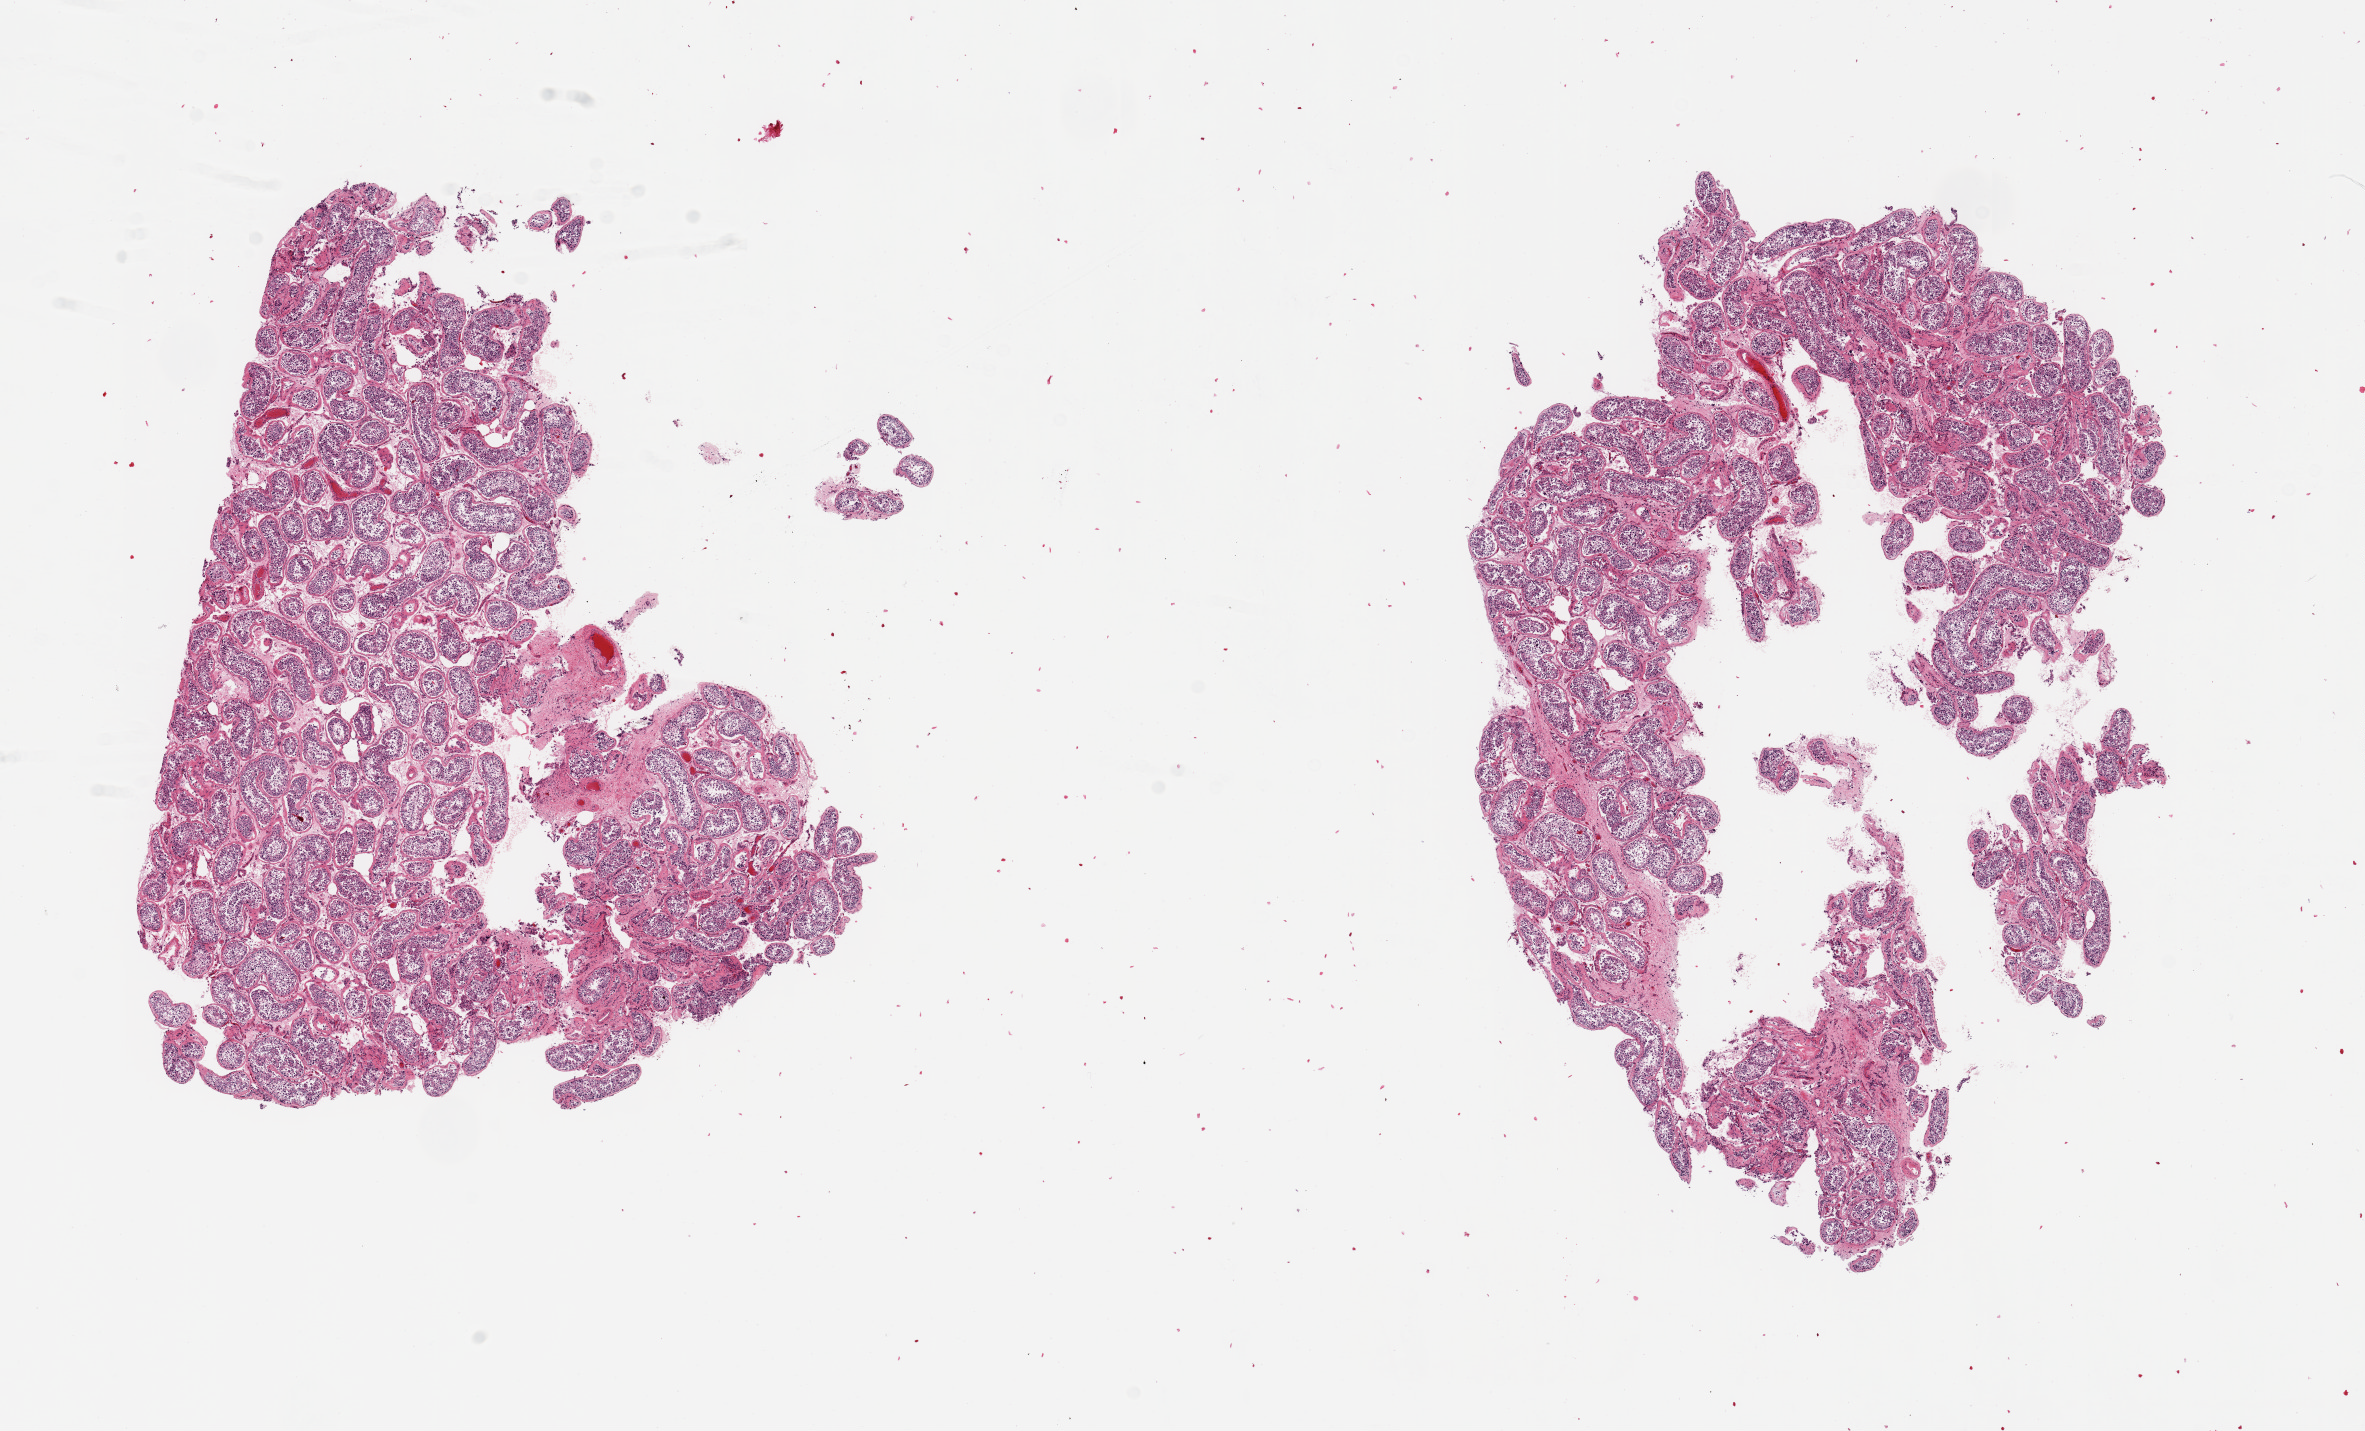
H&E whole-slide image, low-resolution overview of the scanned area, about 18.7 x 11.3 mm (from a 20x scan); PAXgene-fixed, paraffin-embedded tissue; sampled site (target tissue): testis; donor tissue sample.
Pathologist's review note for this sample: 2 pieces 7x6 & 9x6mm; spermatogenesis present, poorly preserved.